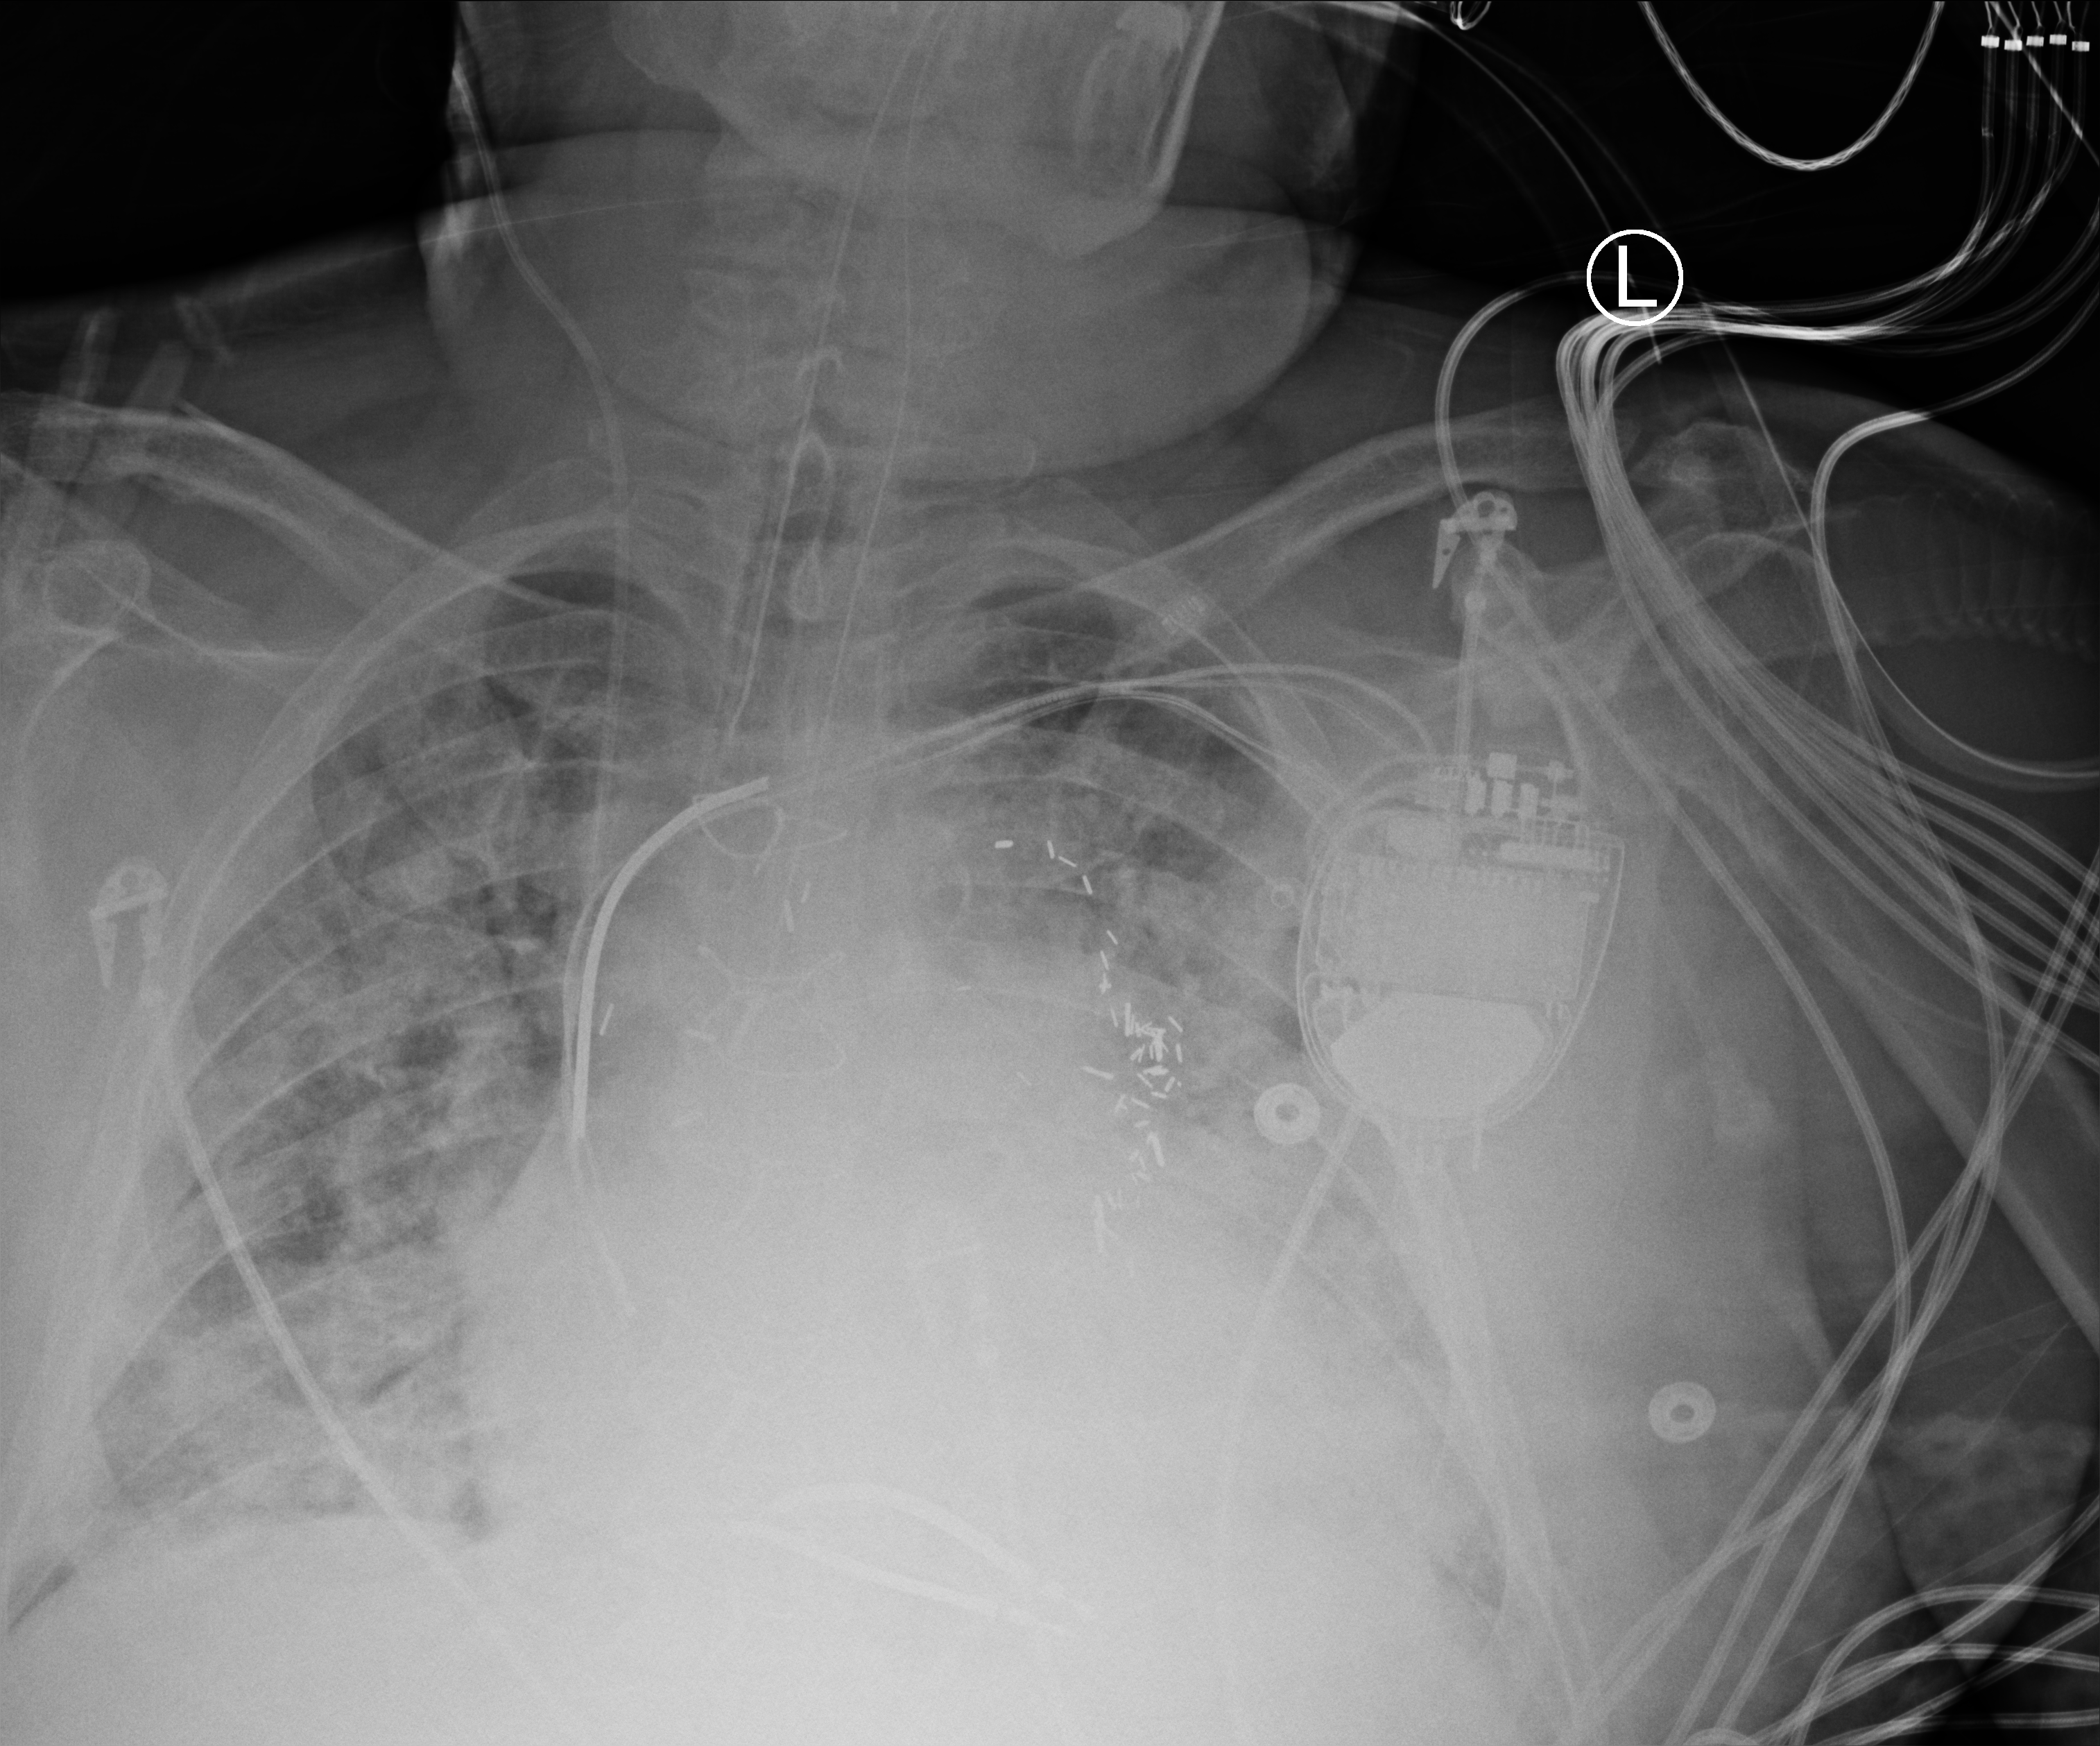
Bedside chest radiograph (computed radiography); anteroposterior (AP) projection. Male patient hospitalised with COVID-19, age 60–74 years.
Admission-level facts for this patient (not findings on this image; timing relative to this image not recorded):
- admitted to intensive care during this hospital stay: yes